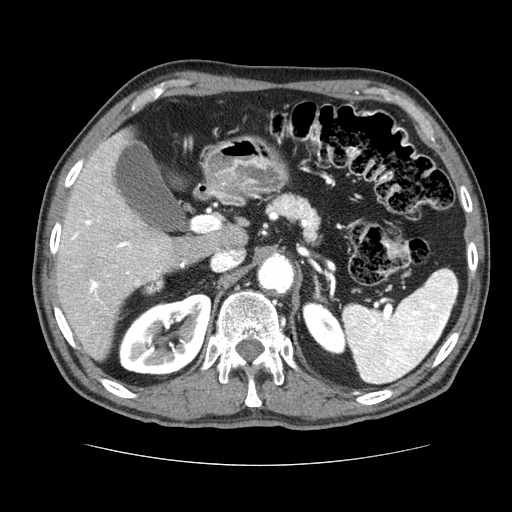
Contrast-enhanced abdominal CT (liver protocol), one axial slice; position 43 of 79 along the scan axis; 120 kVp; soft-tissue window (W 400 / L 40 HU); 2.5 mm slice thickness; 512 × 512 image matrix, field of view 360 × 360 mm. From the clinical record (not read from this slice): diagnosis: hepatocellular carcinoma (patient treated with transarterial chemoembolisation; whether this scan precedes or follows treatment is not stated here); TNM stage (as recorded): Stage-I; Child-Pugh class: A.
Outlined on this slice (semi-automatically segmented with operator editing):
- liver parenchyma outside the tumour (the mass and vessels are separate outlines, so this box may not span the whole liver): box from (x=56, y=130) to (x=176, y=360) px
- liver vessels: (x=62, y=166)–(x=160, y=324)